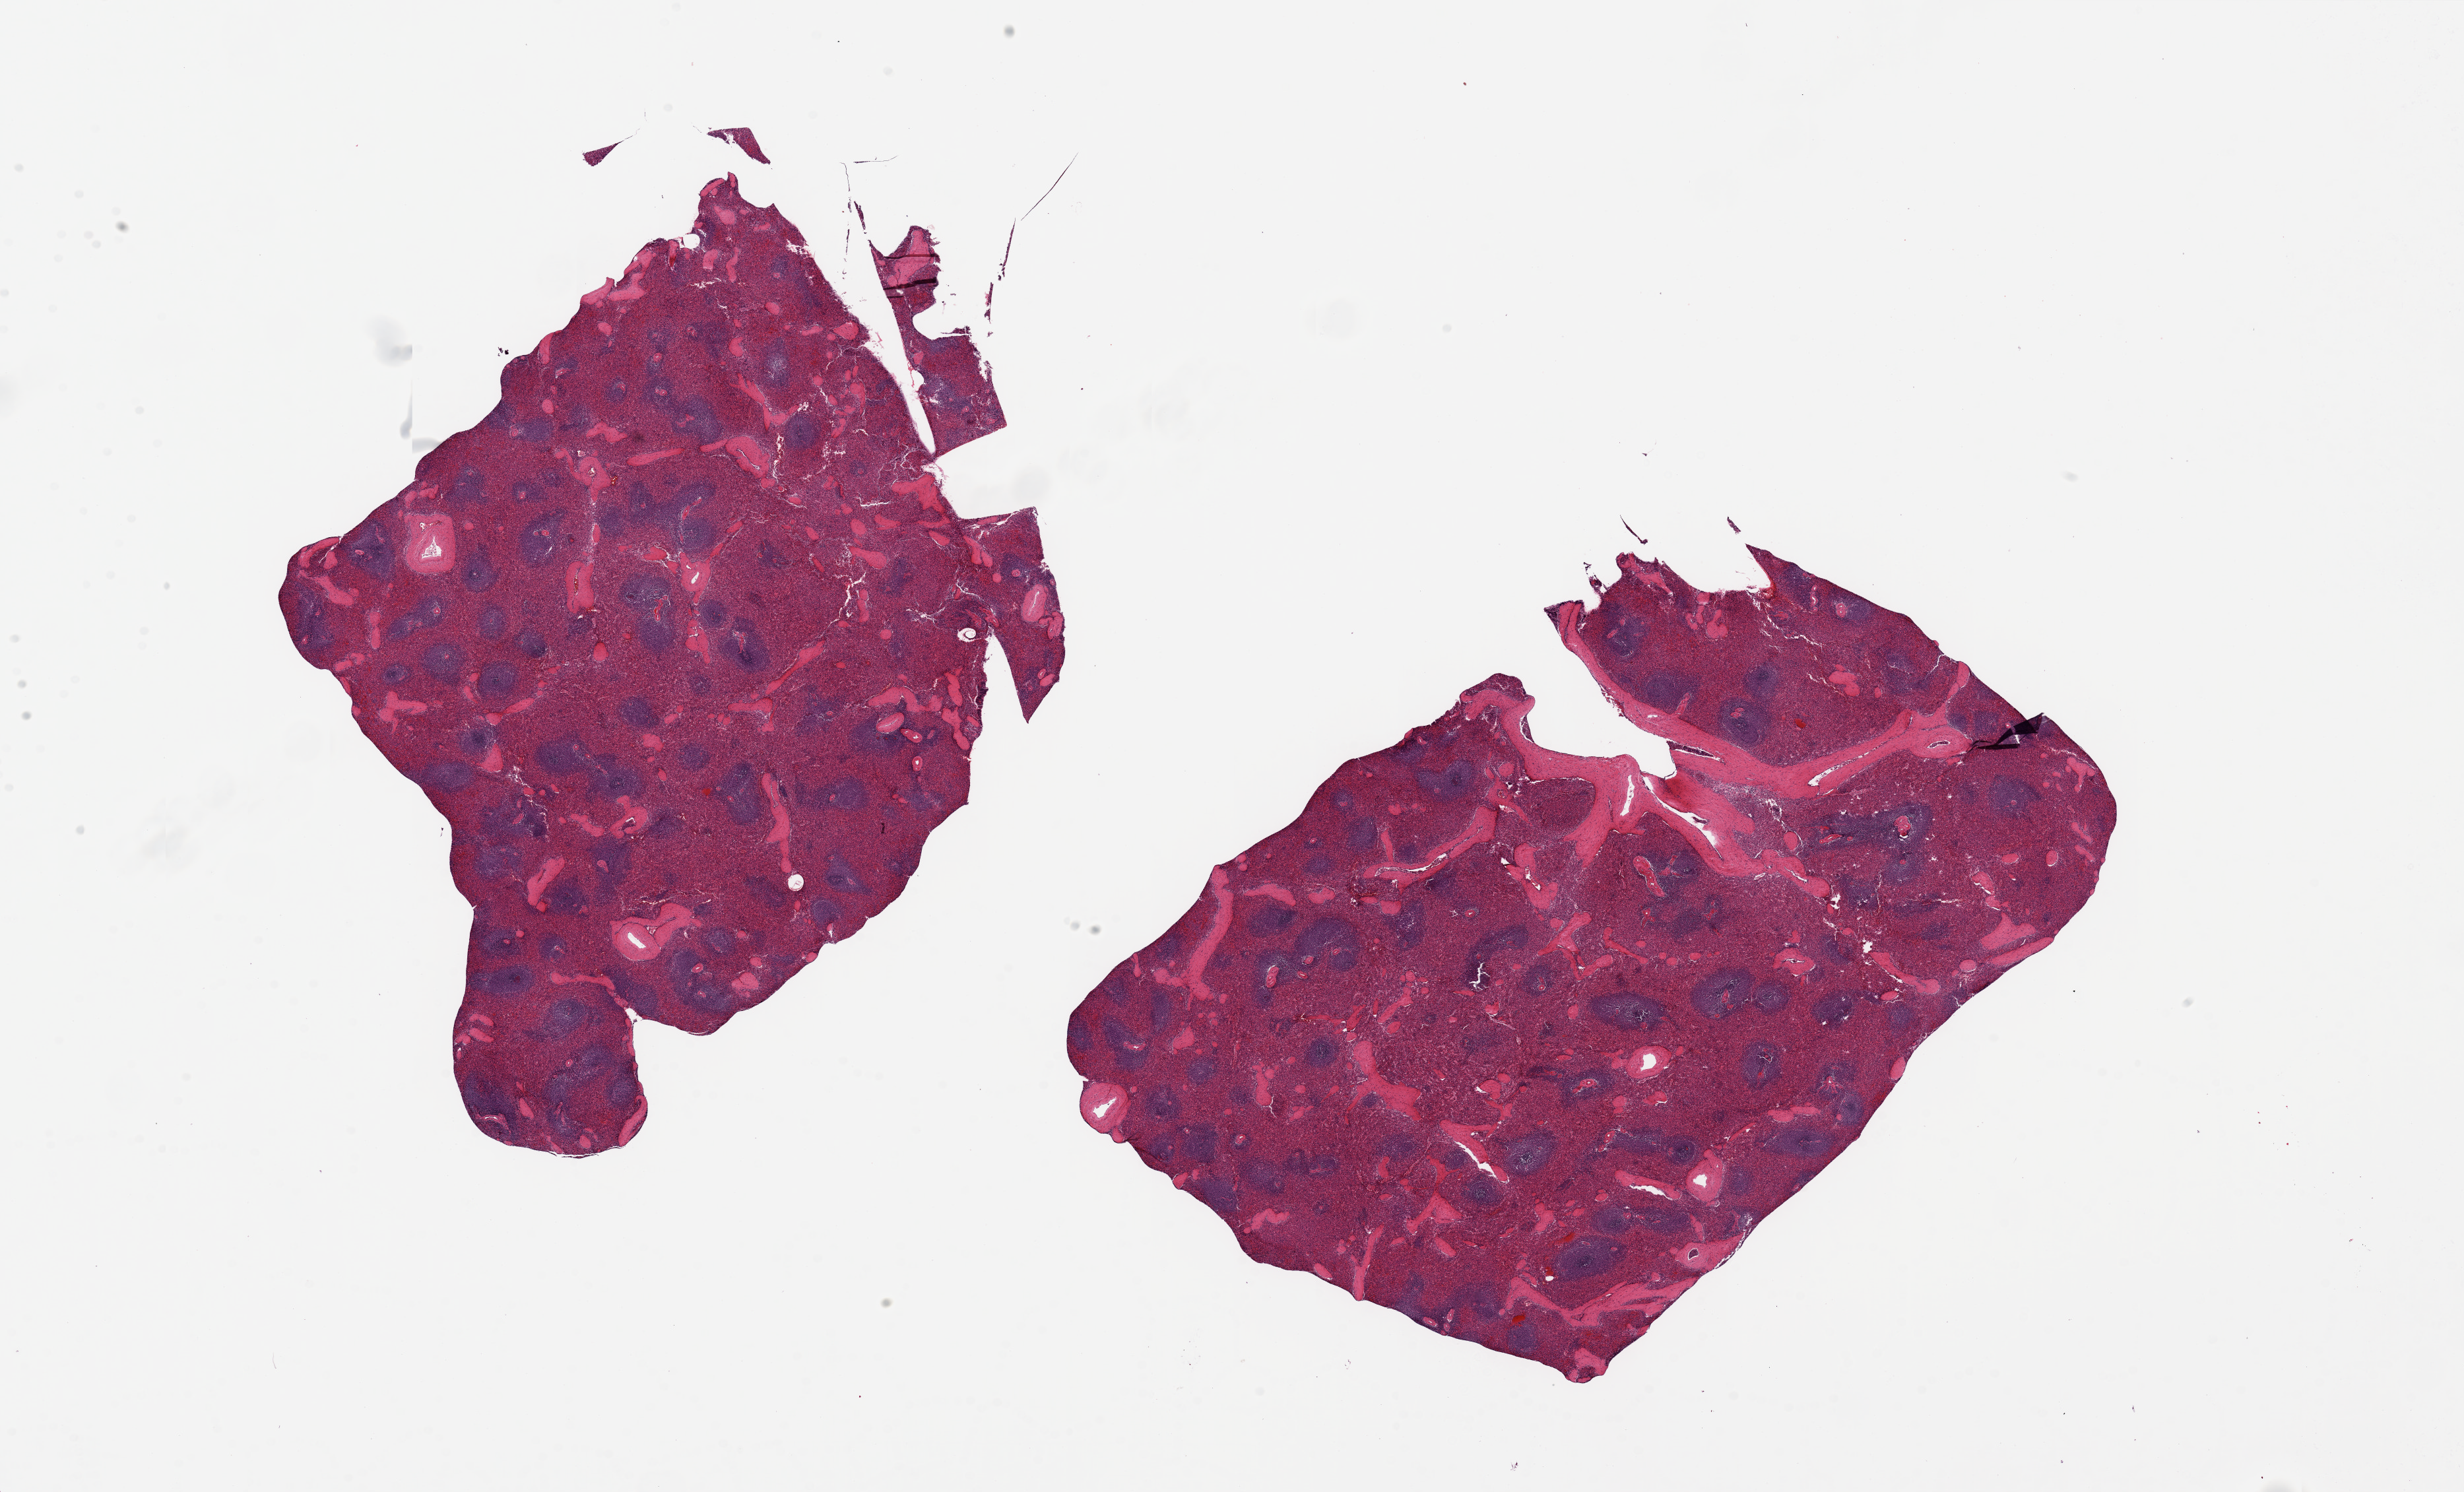
Digitized hematoxylin and eosin (H&E)-stained section, brightfield, low-resolution overview of the scanned area, about 29.5 x 17.9 mm. PAXgene-fixed, paraffin-embedded tissue. Section of spleen (target tissue). Tissue donor sample. Donor sex: male.
• reviewer comment on this tissue sample: 2 pieces ~8x7mm